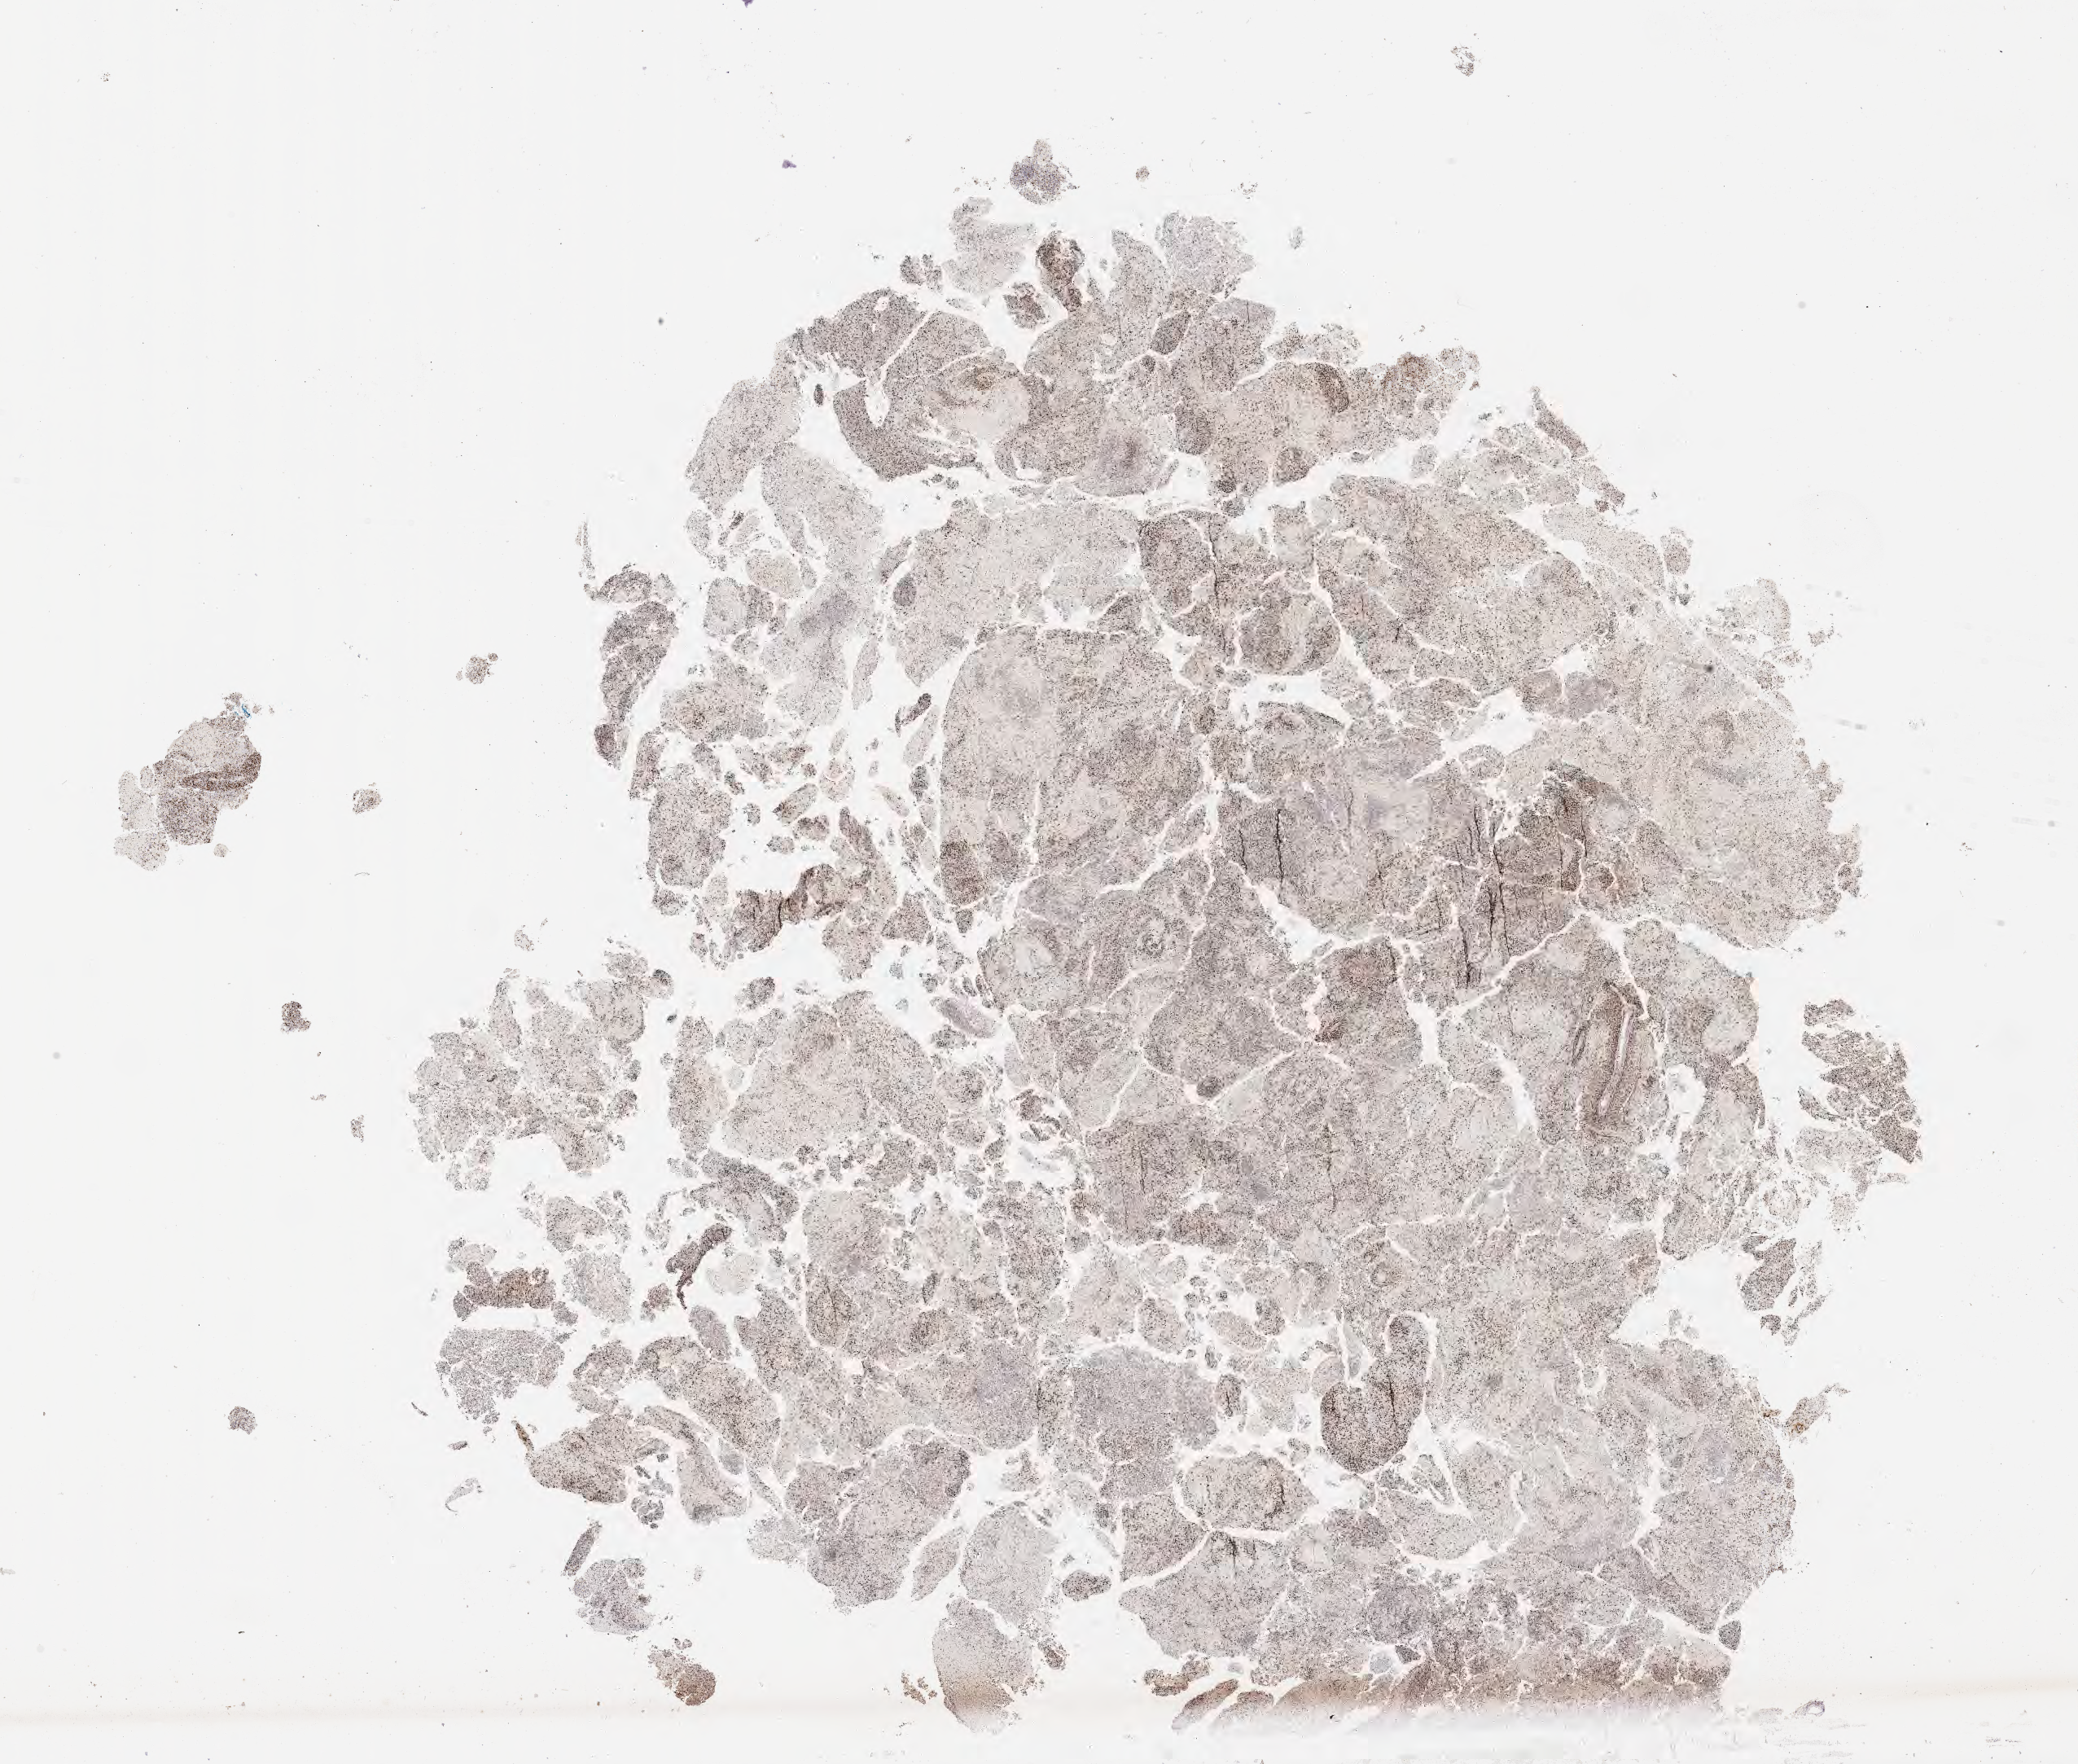
Immunohistochemistry (IHC) whole-slide image stained for Ki-67, whole scanned area (about 20.6 x 17.5 mm) shown as a low-resolution overview, specimen: tumor tissue, site: brain. Patient male; aged 51.
Histologic diagnosis: Diffuse large B-cell lymphoma, NOS.